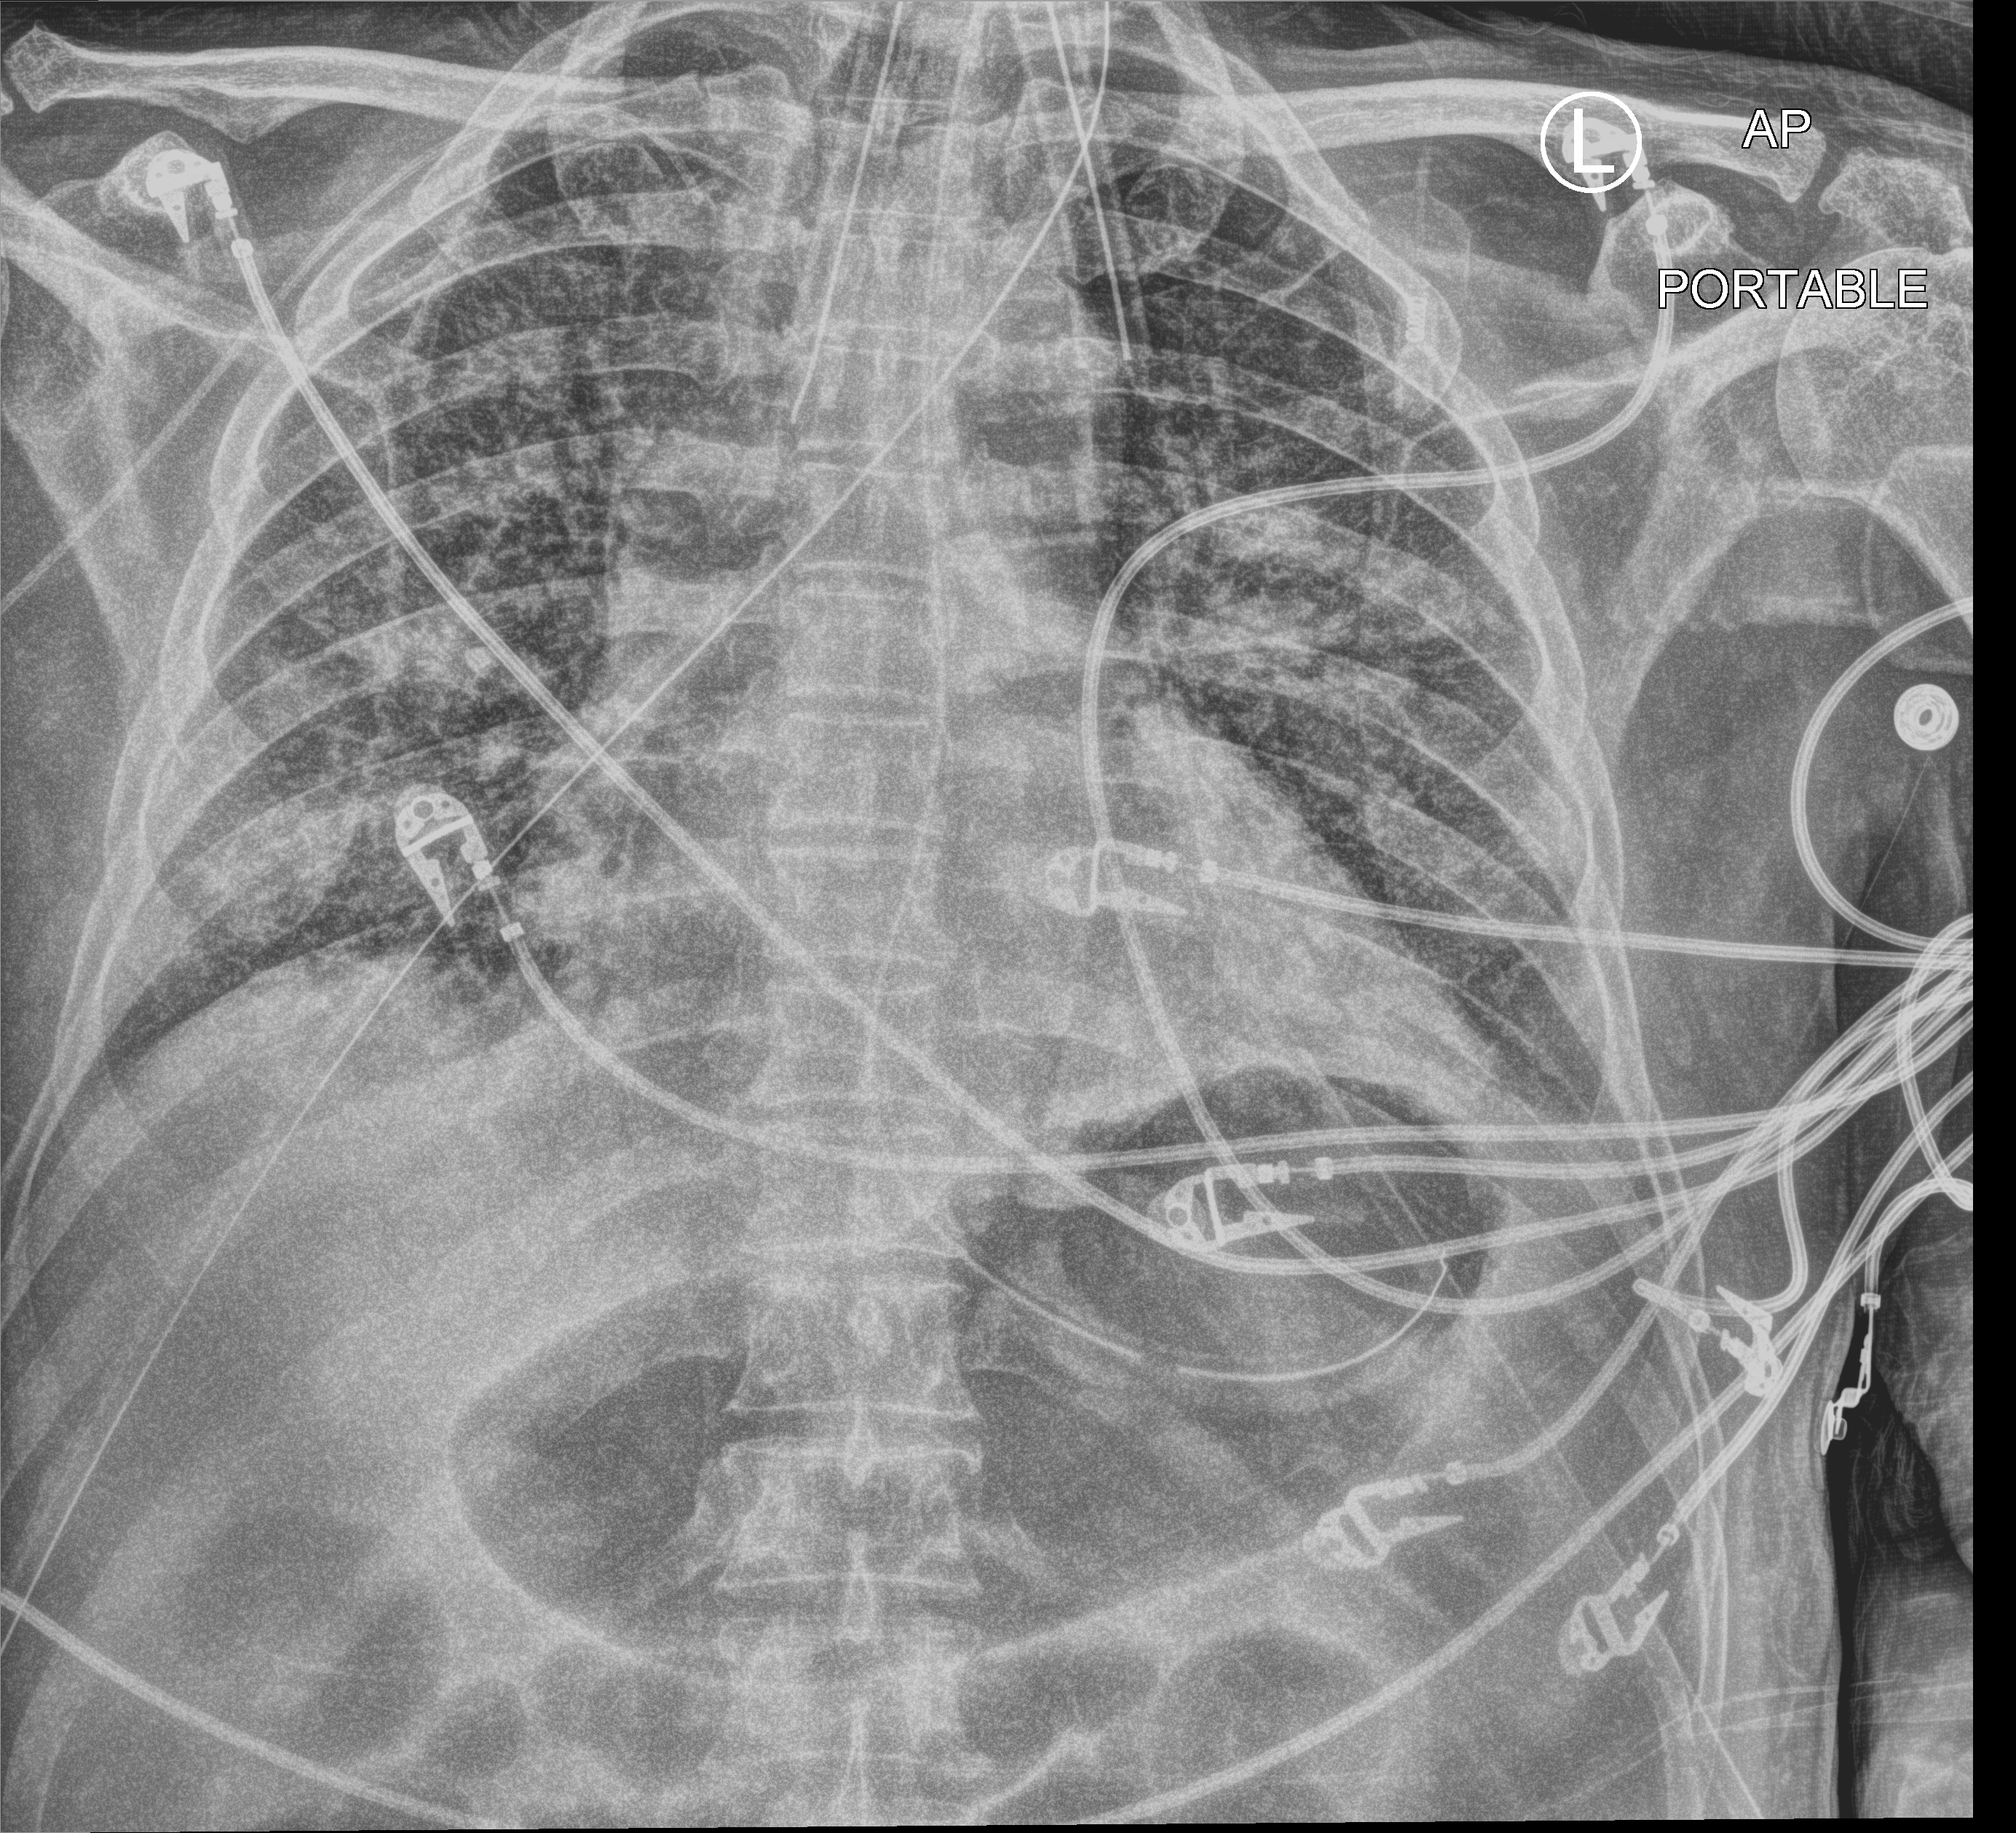
Chest X-ray (portable); anteroposterior (AP) projection. Patient hospitalised with COVID-19; male, aged 60–74 years.
From the hospital-stay record, not from the radiograph (when in the stay this image was taken is not recorded):
- admitted to intensive care during this hospital stay: yes